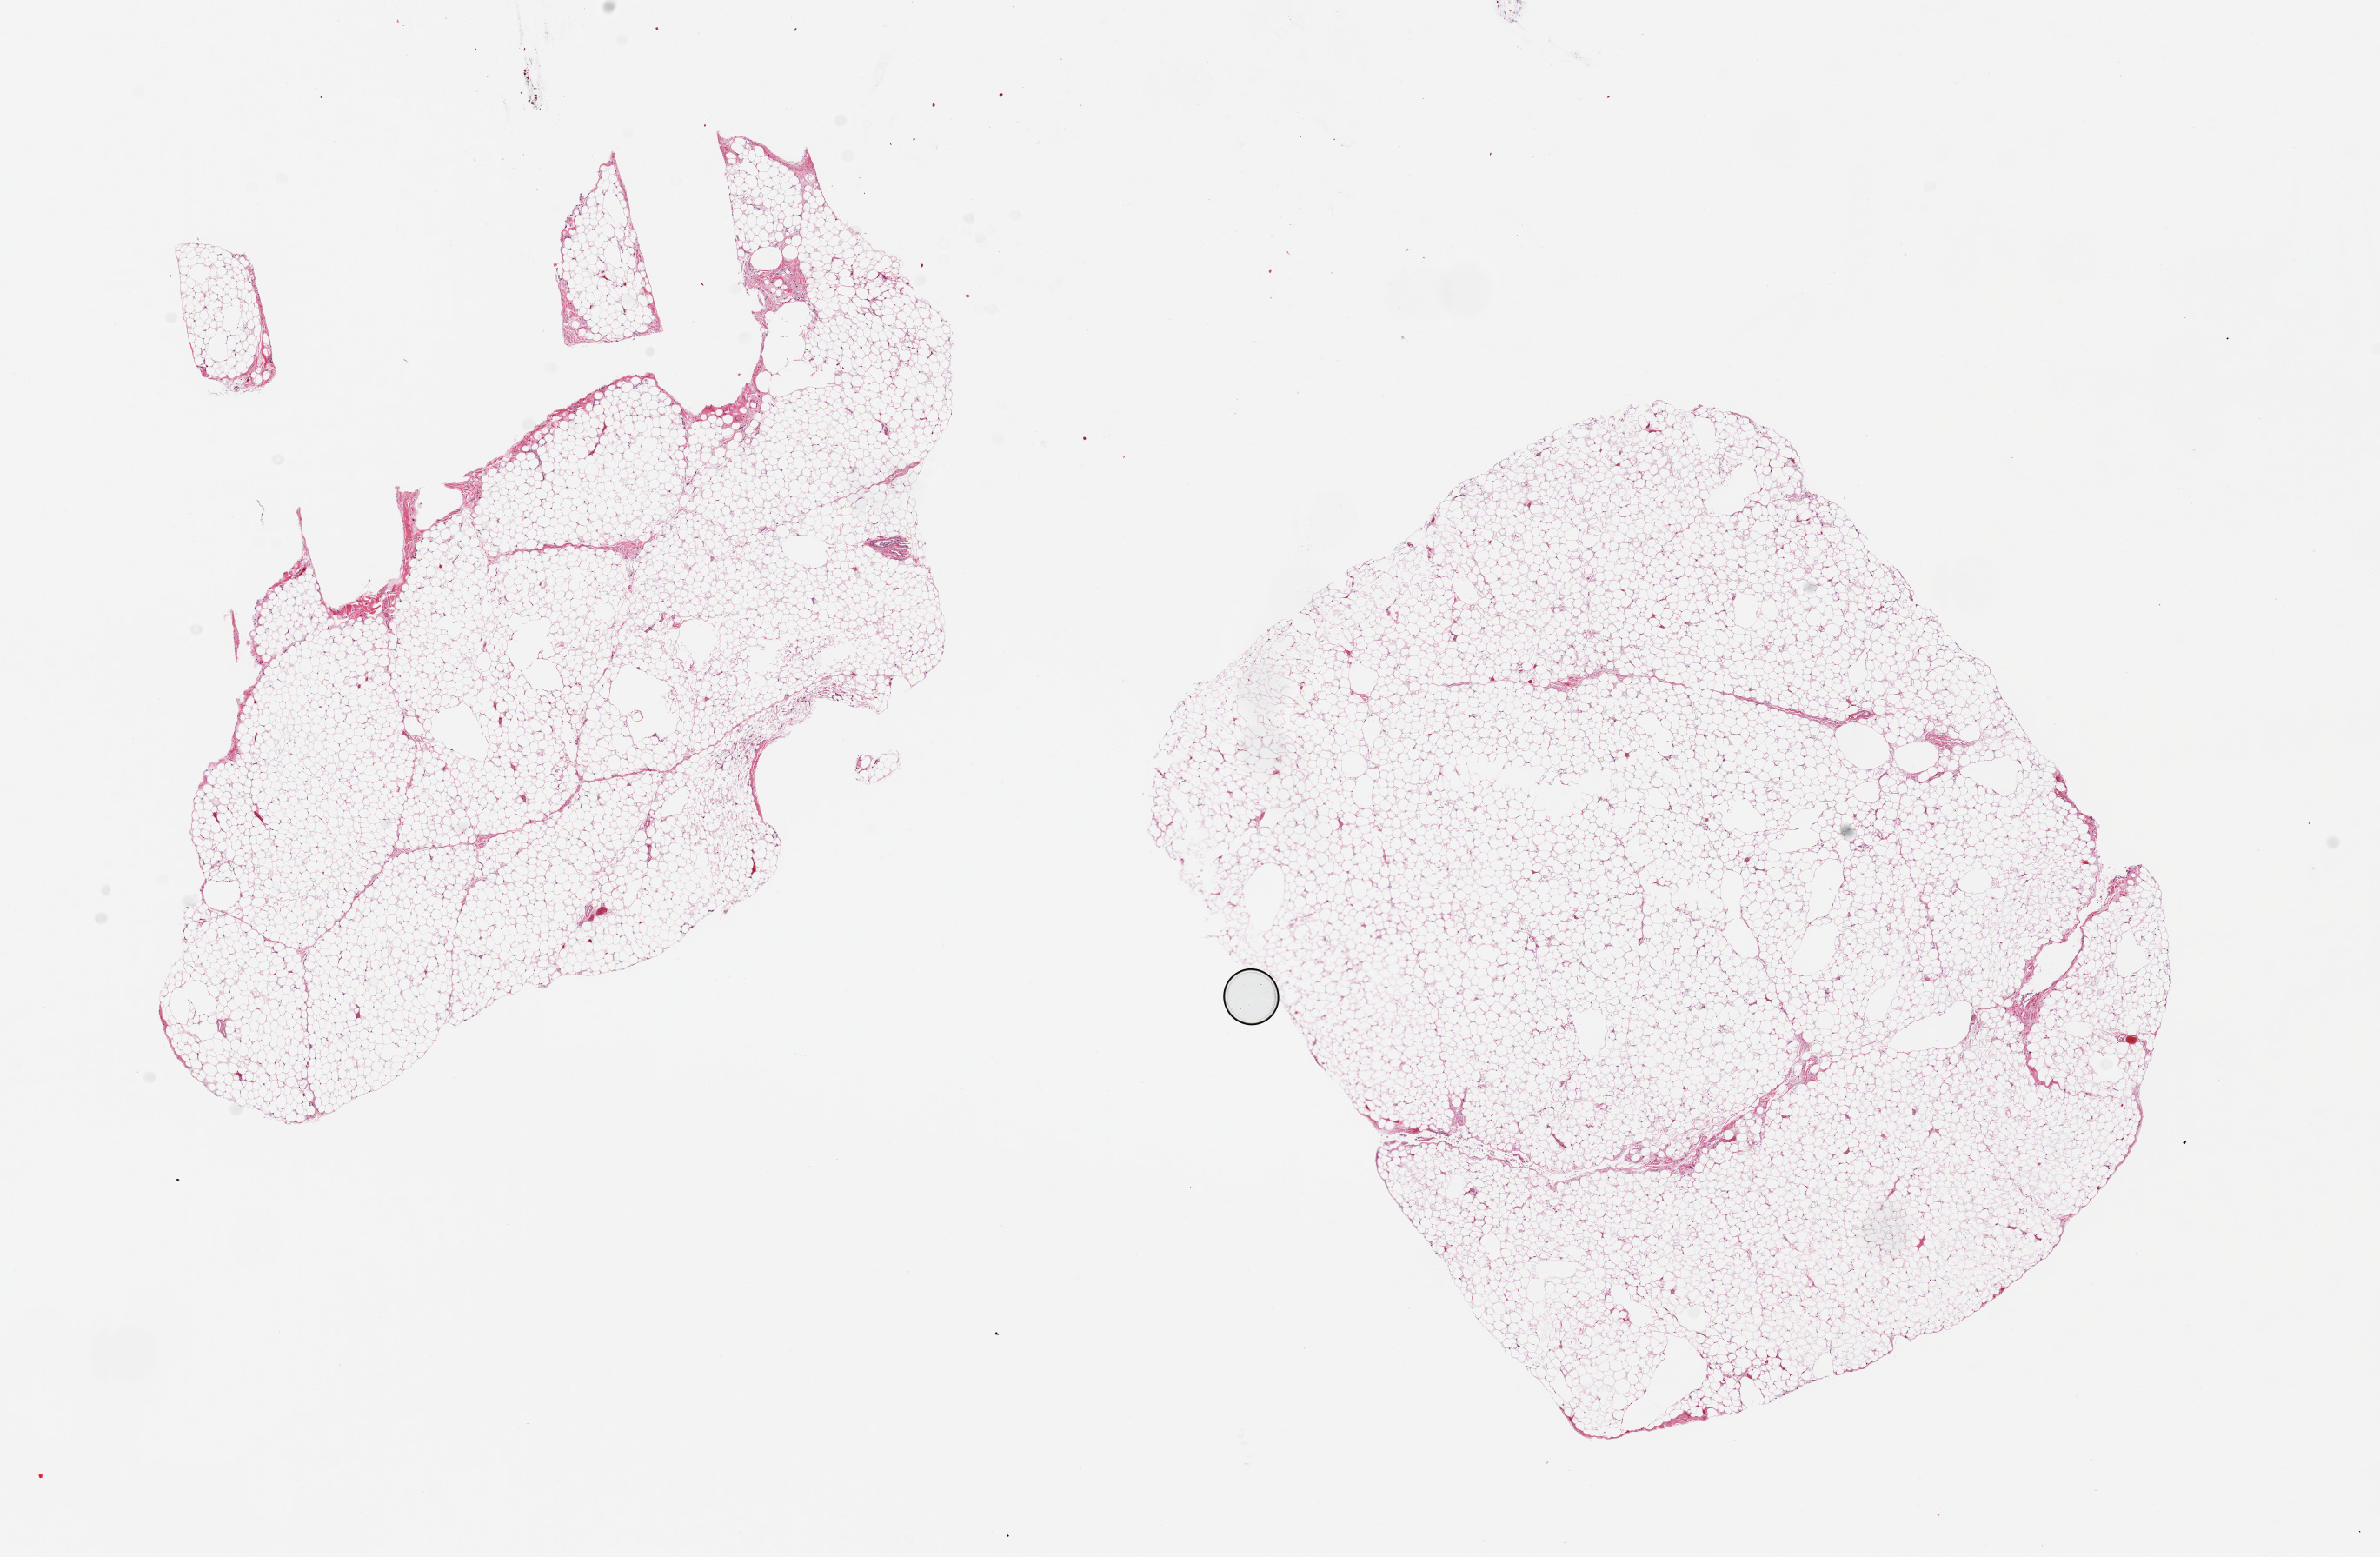
H&E whole-slide image, whole scanned area (about 21.7 x 14.2 mm) shown as a low-resolution overview; PAXgene-fixed paraffin-embedded (PFPE) section; sampled site (target tissue): omentum; tissue donor sample. Donor sex: female.
- pathologist's review note for this sample: 2 pieces, 8.4x7 & 9x4mm; well preserved